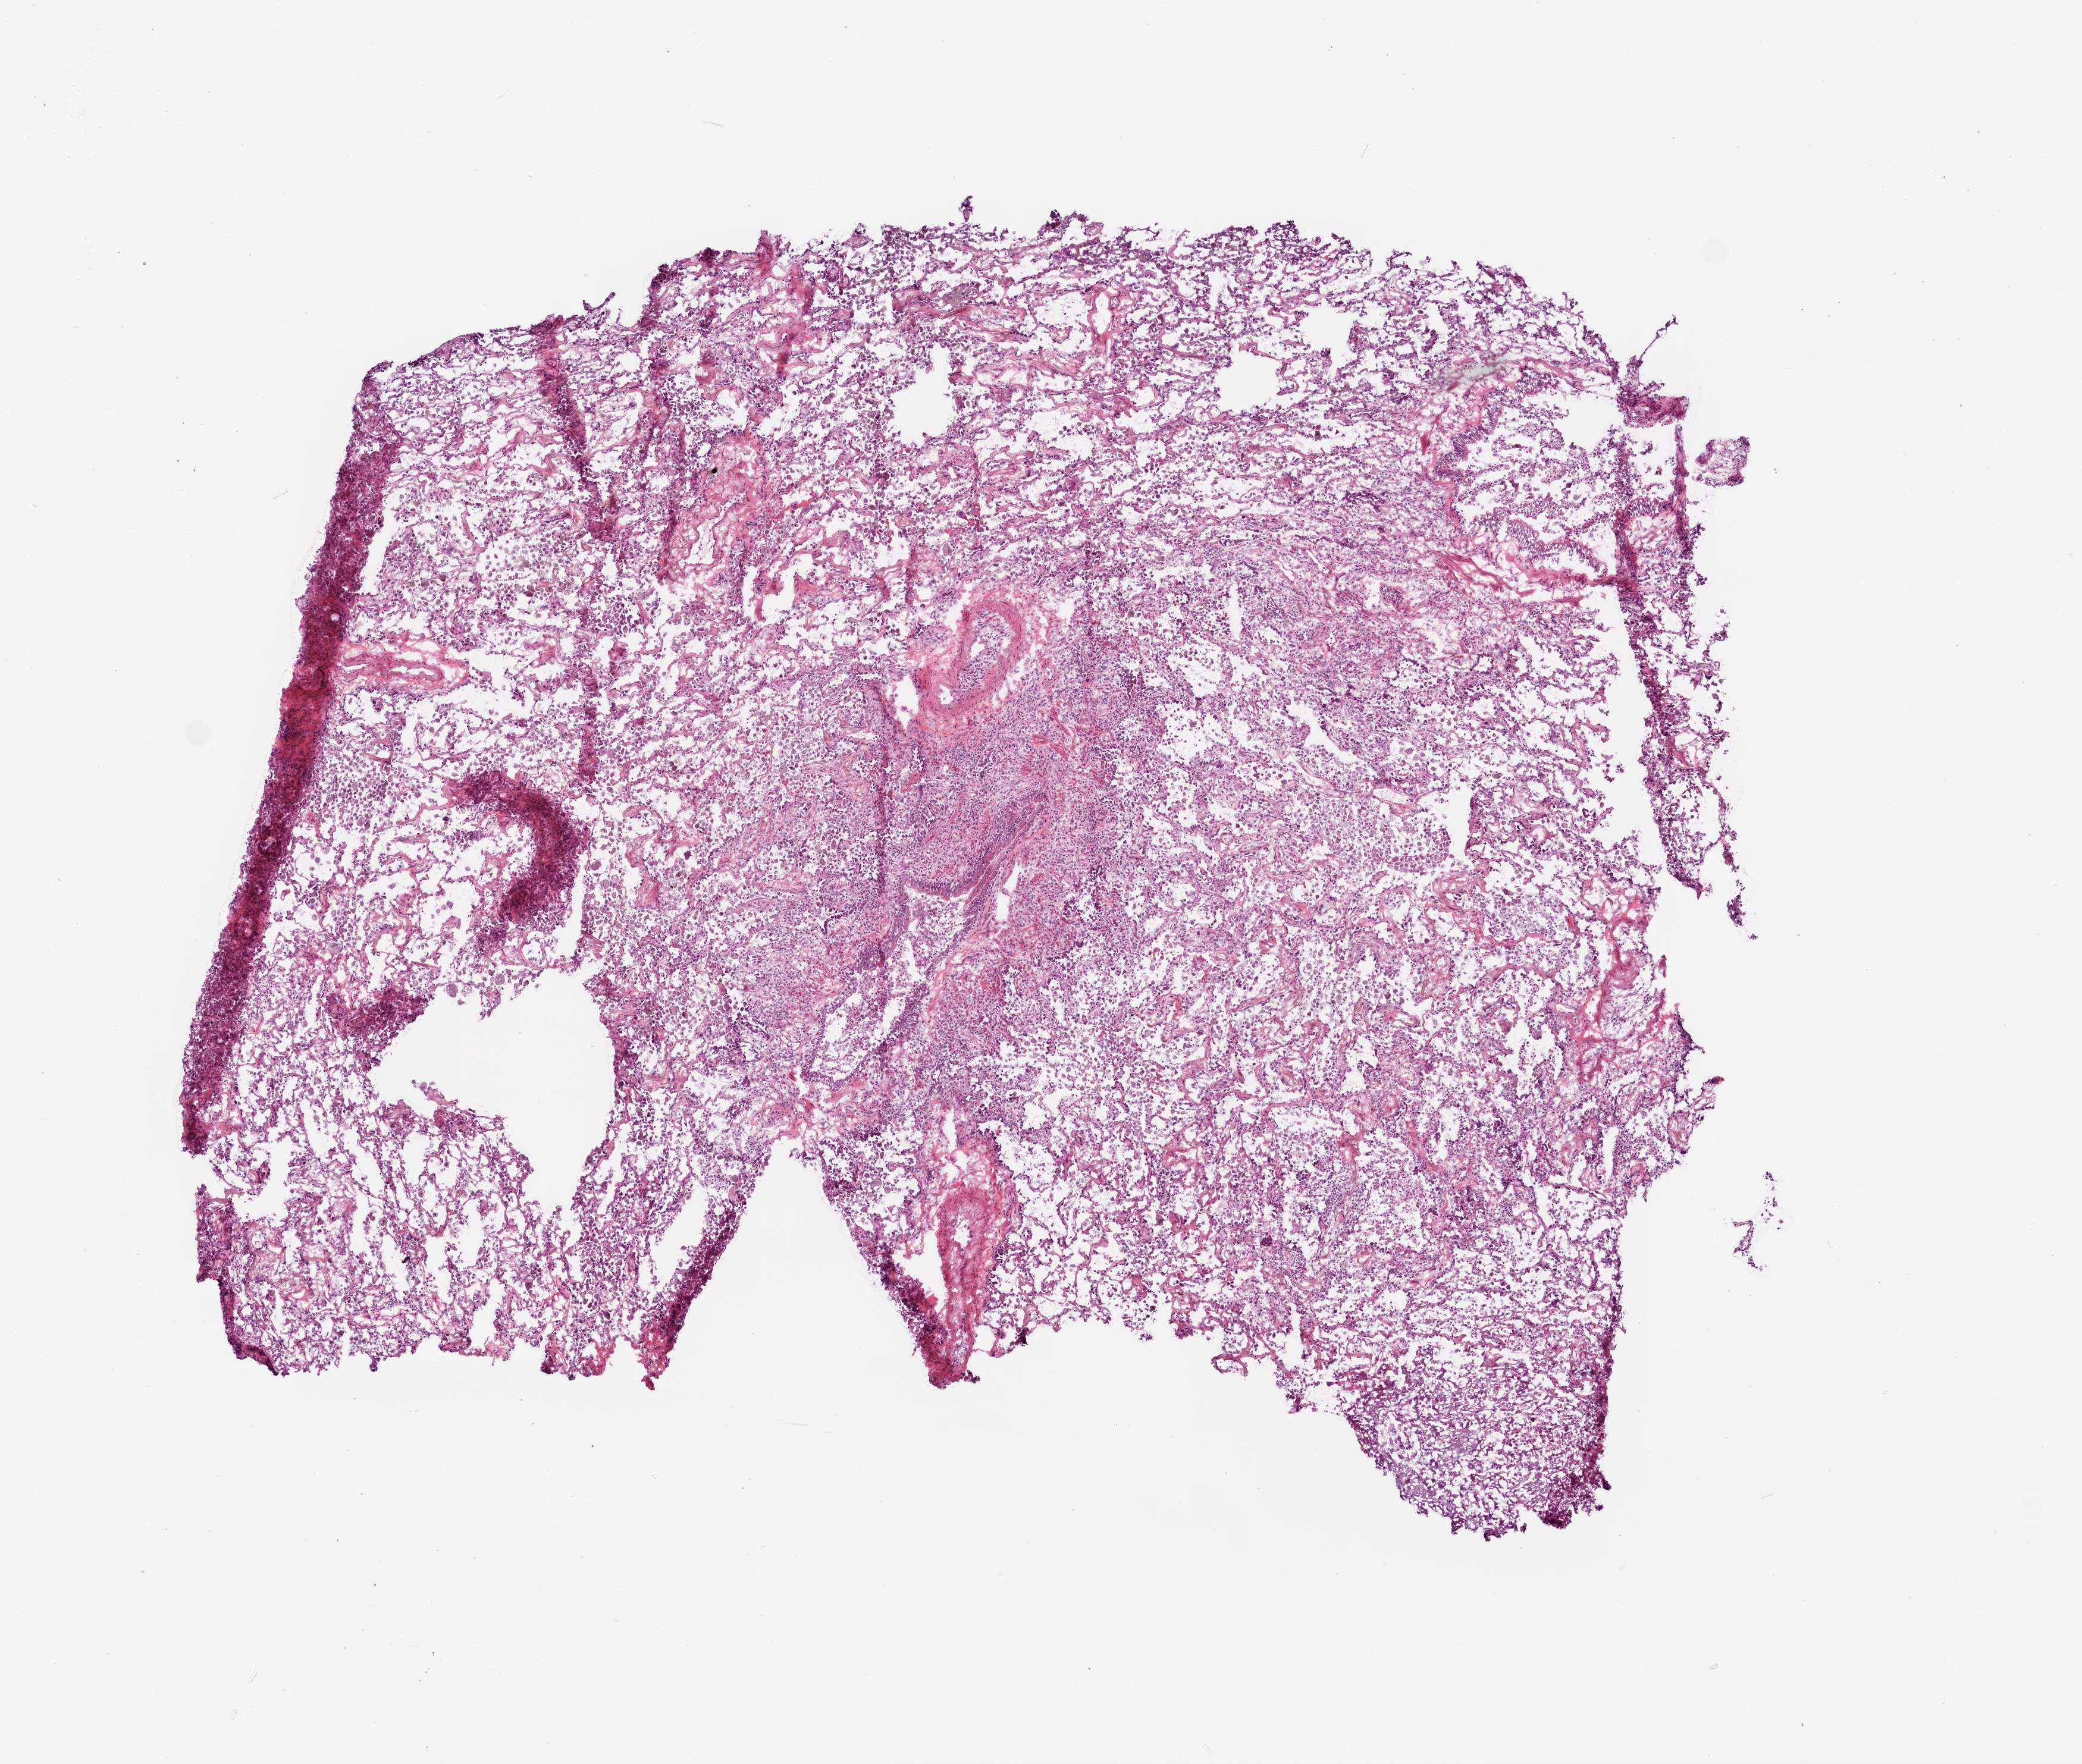
Digitized H&E-stained tissue section (whole slide) — a low-resolution overview of the entire scanned area, about 7.0 x 5.9 mm (slide scanned at 20x), frozen section, lung, primary tumour sample. Patient sex: female. Slide review estimates, as recorded: tumour cells 5%, tumour nuclei 5%, normal cells 95%, stromal cells 0%, necrosis 0%.
AJCC pathologic stage: IIIA. Laterality: left. Diagnosis: Papillary adenocarcinoma, NOS (upper lobe, lung).